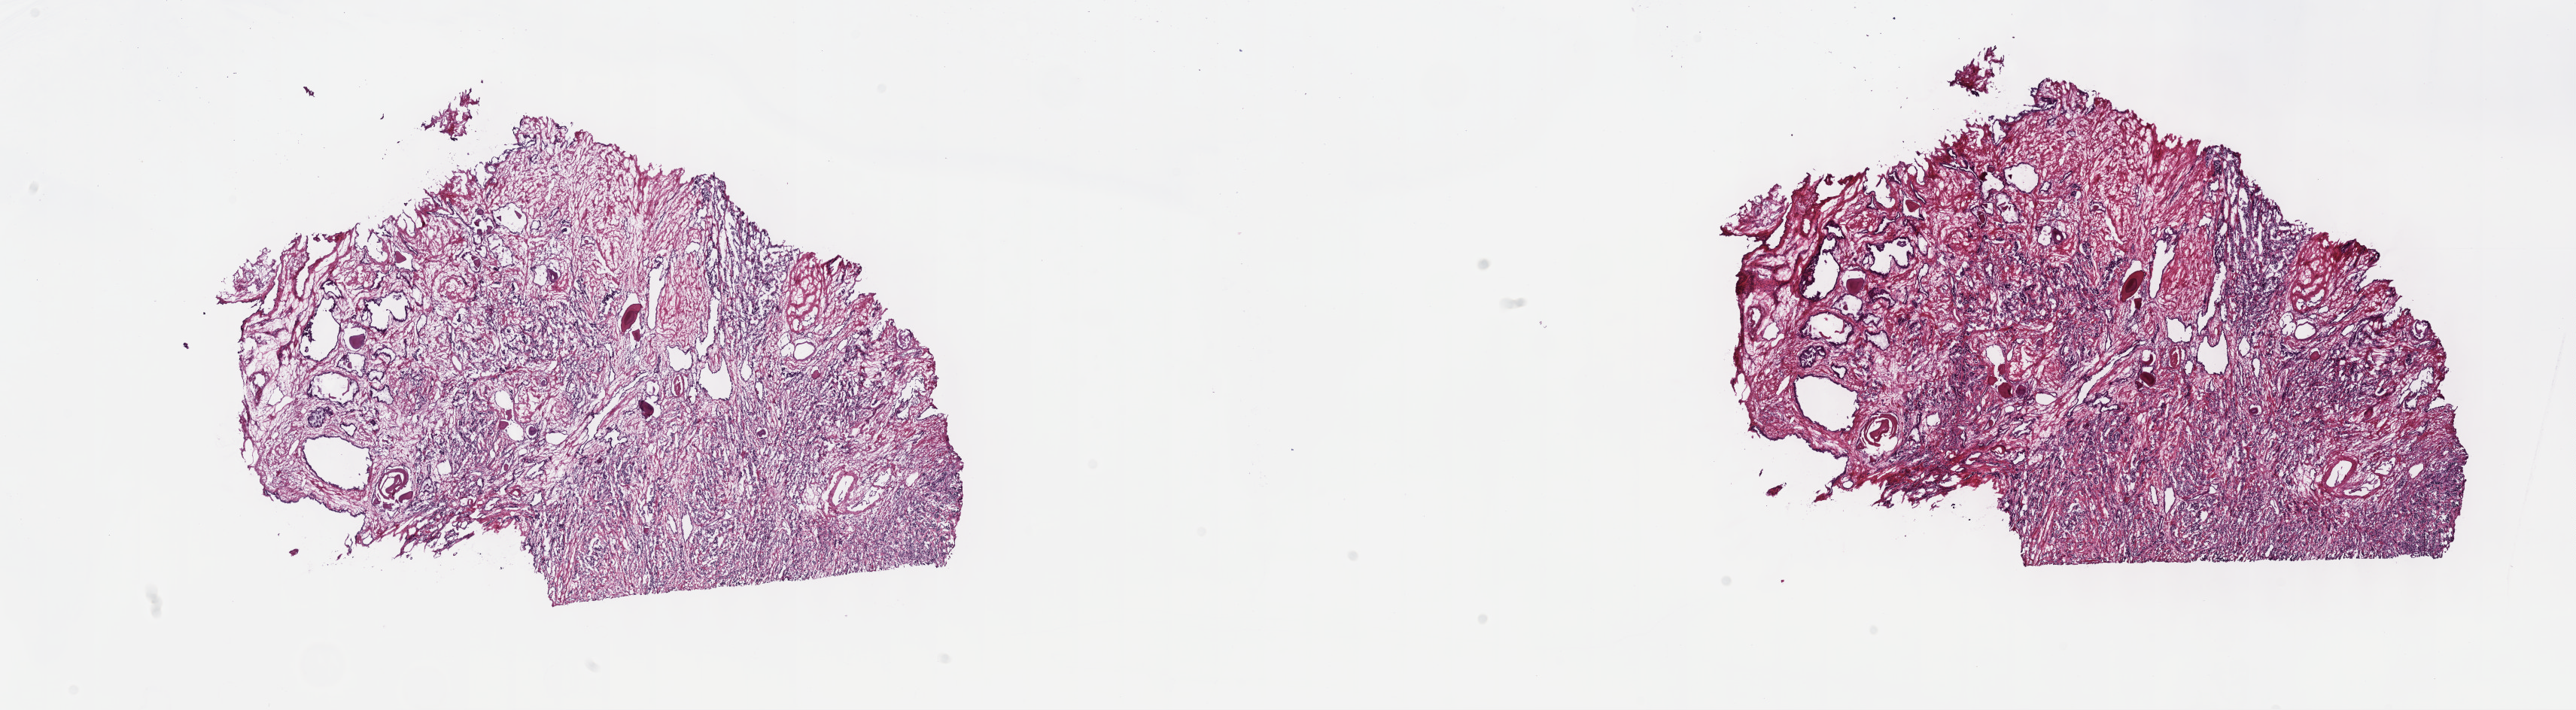
Whole-slide histology image, Hematoxylin and eosin (H&E) stained — shown as a low-resolution overview of the whole scanned area (about 27.7 x 7.6 mm, acquisition: 40x scan). Frozen section from the top of the tissue portion. Primary tumour sample from the prostate. Male, age 65 years at initial diagnosis. Gleason score: 9 (4+5). Slide review estimates, as recorded: tumour cells 40%, tumour nuclei 60%, normal cells 10%, stromal cells 50%, necrosis 0%. Inflammatory infiltration, as recorded: lymphocyte infiltration 0%, monocyte infiltration 0%, neutrophil infiltration 0%.
Laterality: right. Lymph nodes positive (case pathology): 0 of 3 examined. Diagnosis: Adenocarcinoma, NOS (prostate gland).